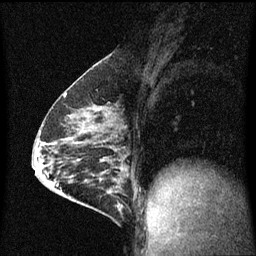
Breast MRI (dynamic contrast-enhanced), one sagittal slice. Position 33 of 60 along the scan axis. Dynamic contrast-enhanced series, image 2 of 3 at this slice position (ordered by acquisition). 1.5 T. TE 4.2 ms, TR 8 ms. 2 mm slice thickness. 256 × 256 image matrix, field of view 200 × 200 mm. Patient: female, 64 years.
Structures marked on this image (semi-automatic segmentation, software-assisted and operator-edited):
- analysis volume of interest (the breast-tissue region the enhancement analysis was run in; not a lesion): bounding box [x1, y1, x2, y2] px = [87, 176, 128, 217]
- tumour enhancement mask (voxels above the 70 % enhancement threshold inside the analysis volume of interest): [93, 176, 122, 211]